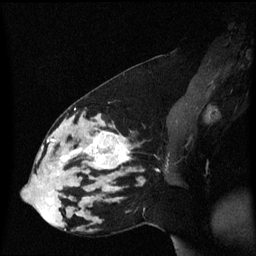
Breast MRI (dynamic contrast-enhanced), one sagittal slice; slice 26 of 60 in the series (ordered by position); dynamic contrast-enhanced series, image 2 of 3 at this slice position (ordered by acquisition); 1.5 T; TE 4.2 ms, TR 8.4 ms; 2 mm slice thickness; 256 × 256 image matrix. Female patient, age 33 years. Case-level facts recorded for this patient, not image findings: setting: breast cancer imaged before/during neoadjuvant chemotherapy; receptor status: triple-negative.
Outlined on this slice (semi-automatically segmented with operator editing):
- analysis volume of interest (the breast-tissue region the enhancement analysis was run in; not a lesion): bounding box (x1, y1, x2, y2) in pixels: (44, 123, 139, 189)
- tumour enhancement mask (voxels above the 70 % enhancement threshold inside the analysis volume of interest): (54, 132, 131, 170)